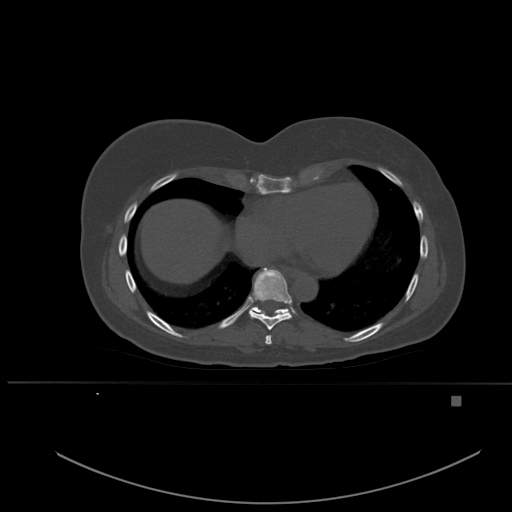
CT including the spine, one axial slice. Slice 317 of 651 in the series (ordered by position). Bone window (W 1800 / L 400 HU). 1.5 mm slice thickness. 512 × 512 image matrix. Patient: female, 49 years. From the clinical record (not read from this slice): primary cancer: breast.
Structures marked on this image (semi-automatically segmented with operator editing):
- T7 vertebra: bounding box <265,335,272,345> (left, top, right, bottom; pixels)
- T8 vertebra: <249,268,292,330>
- T9 vertebra: <249,307,289,313>